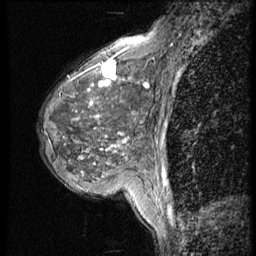
Breast MRI (dynamic contrast-enhanced), one sagittal slice; position 17 of 56 along the scan axis; 4 images stored at this slice position (order not interpretable as contrast timing); 1.5 T; TE 4.2 ms, TR 9 ms; 2.5 mm slice thickness; 256 × 256 image matrix, field of view 180 × 180 mm. Patient: female, 50 years. Case-level facts recorded for this patient, not image findings: setting: breast cancer imaged before/during neoadjuvant chemotherapy; receptor status: triple-negative.
Outlined on this slice (semi-automatic segmentation, software-assisted and operator-edited):
- analysis volume of interest (the breast-tissue region the enhancement analysis was run in; not a lesion): box from (x=36, y=46) to (x=148, y=188) px
- tumour enhancement mask (voxels above the 140 % enhancement threshold inside the analysis volume of interest): (x=92, y=61)–(x=125, y=118)